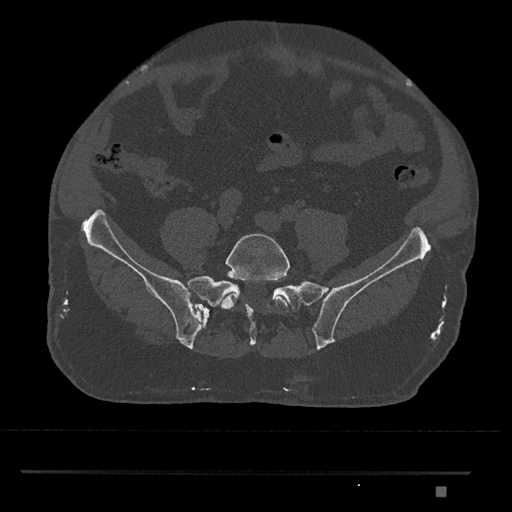
CT including the spine, one axial slice. Slice 532 of 1134 in the series (ordered by position). 120 kVp. Bone window (W 1800 / L 400 HU). 0.5 mm slice thickness. 512 × 512 image matrix, field of view 429 × 429 mm. Male patient, age 65 years. Case-level facts recorded for this patient, not image findings: primary cancer: prostate.
Outlined on this slice (semi-automatically segmented with operator editing):
- L5 vertebra: box from (x=220, y=233) to (x=290, y=313) px